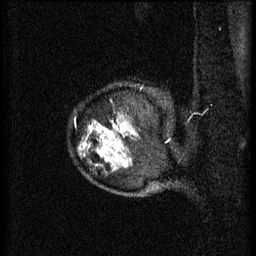
Breast MRI (dynamic contrast-enhanced), one sagittal slice; slice 56 of 60 in the series (ordered by position); 3 images stored at this slice position (order not interpretable as contrast timing); 1.5 T; TE 4.2 ms, TR 11 ms; 2 mm slice thickness; 256 × 256 image matrix, field of view 180 × 180 mm. Female patient, age 52 years.
Annotated regions visible in this slice (semi-automatic segmentation, software-assisted and operator-edited):
- analysis volume of interest (the breast-tissue region the enhancement analysis was run in; not a lesion): bounding box (x1, y1, x2, y2) in pixels: (81, 100, 170, 157)
- tumour enhancement mask (voxels above the 70 % enhancement threshold inside the analysis volume of interest): (85, 120, 134, 155)